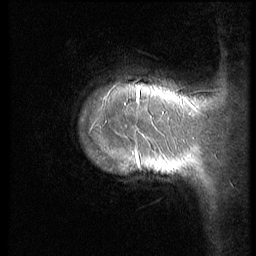
Breast MRI (dynamic contrast-enhanced), one sagittal slice. Slice 9 of 70 in the series (ordered by position). 3 images stored at this slice position (order not interpretable as contrast timing). 1.5 T. TE 4.2 ms, TR 9 ms. 2.5 mm slice thickness. 256 × 256 image matrix, field of view 180 × 180 mm. Female patient, age 28 years. Case-level facts recorded for this patient, not image findings: setting: breast cancer imaged before/during neoadjuvant chemotherapy.
Annotated regions visible in this slice (semi-automatic segmentation, software-assisted and operator-edited):
- analysis volume of interest (the breast-tissue region the enhancement analysis was run in; not a lesion): bounding box <76,50,186,209> (left, top, right, bottom; pixels)
- tumour enhancement mask (voxels above the 140 % enhancement threshold inside the analysis volume of interest): <137,90,142,171>